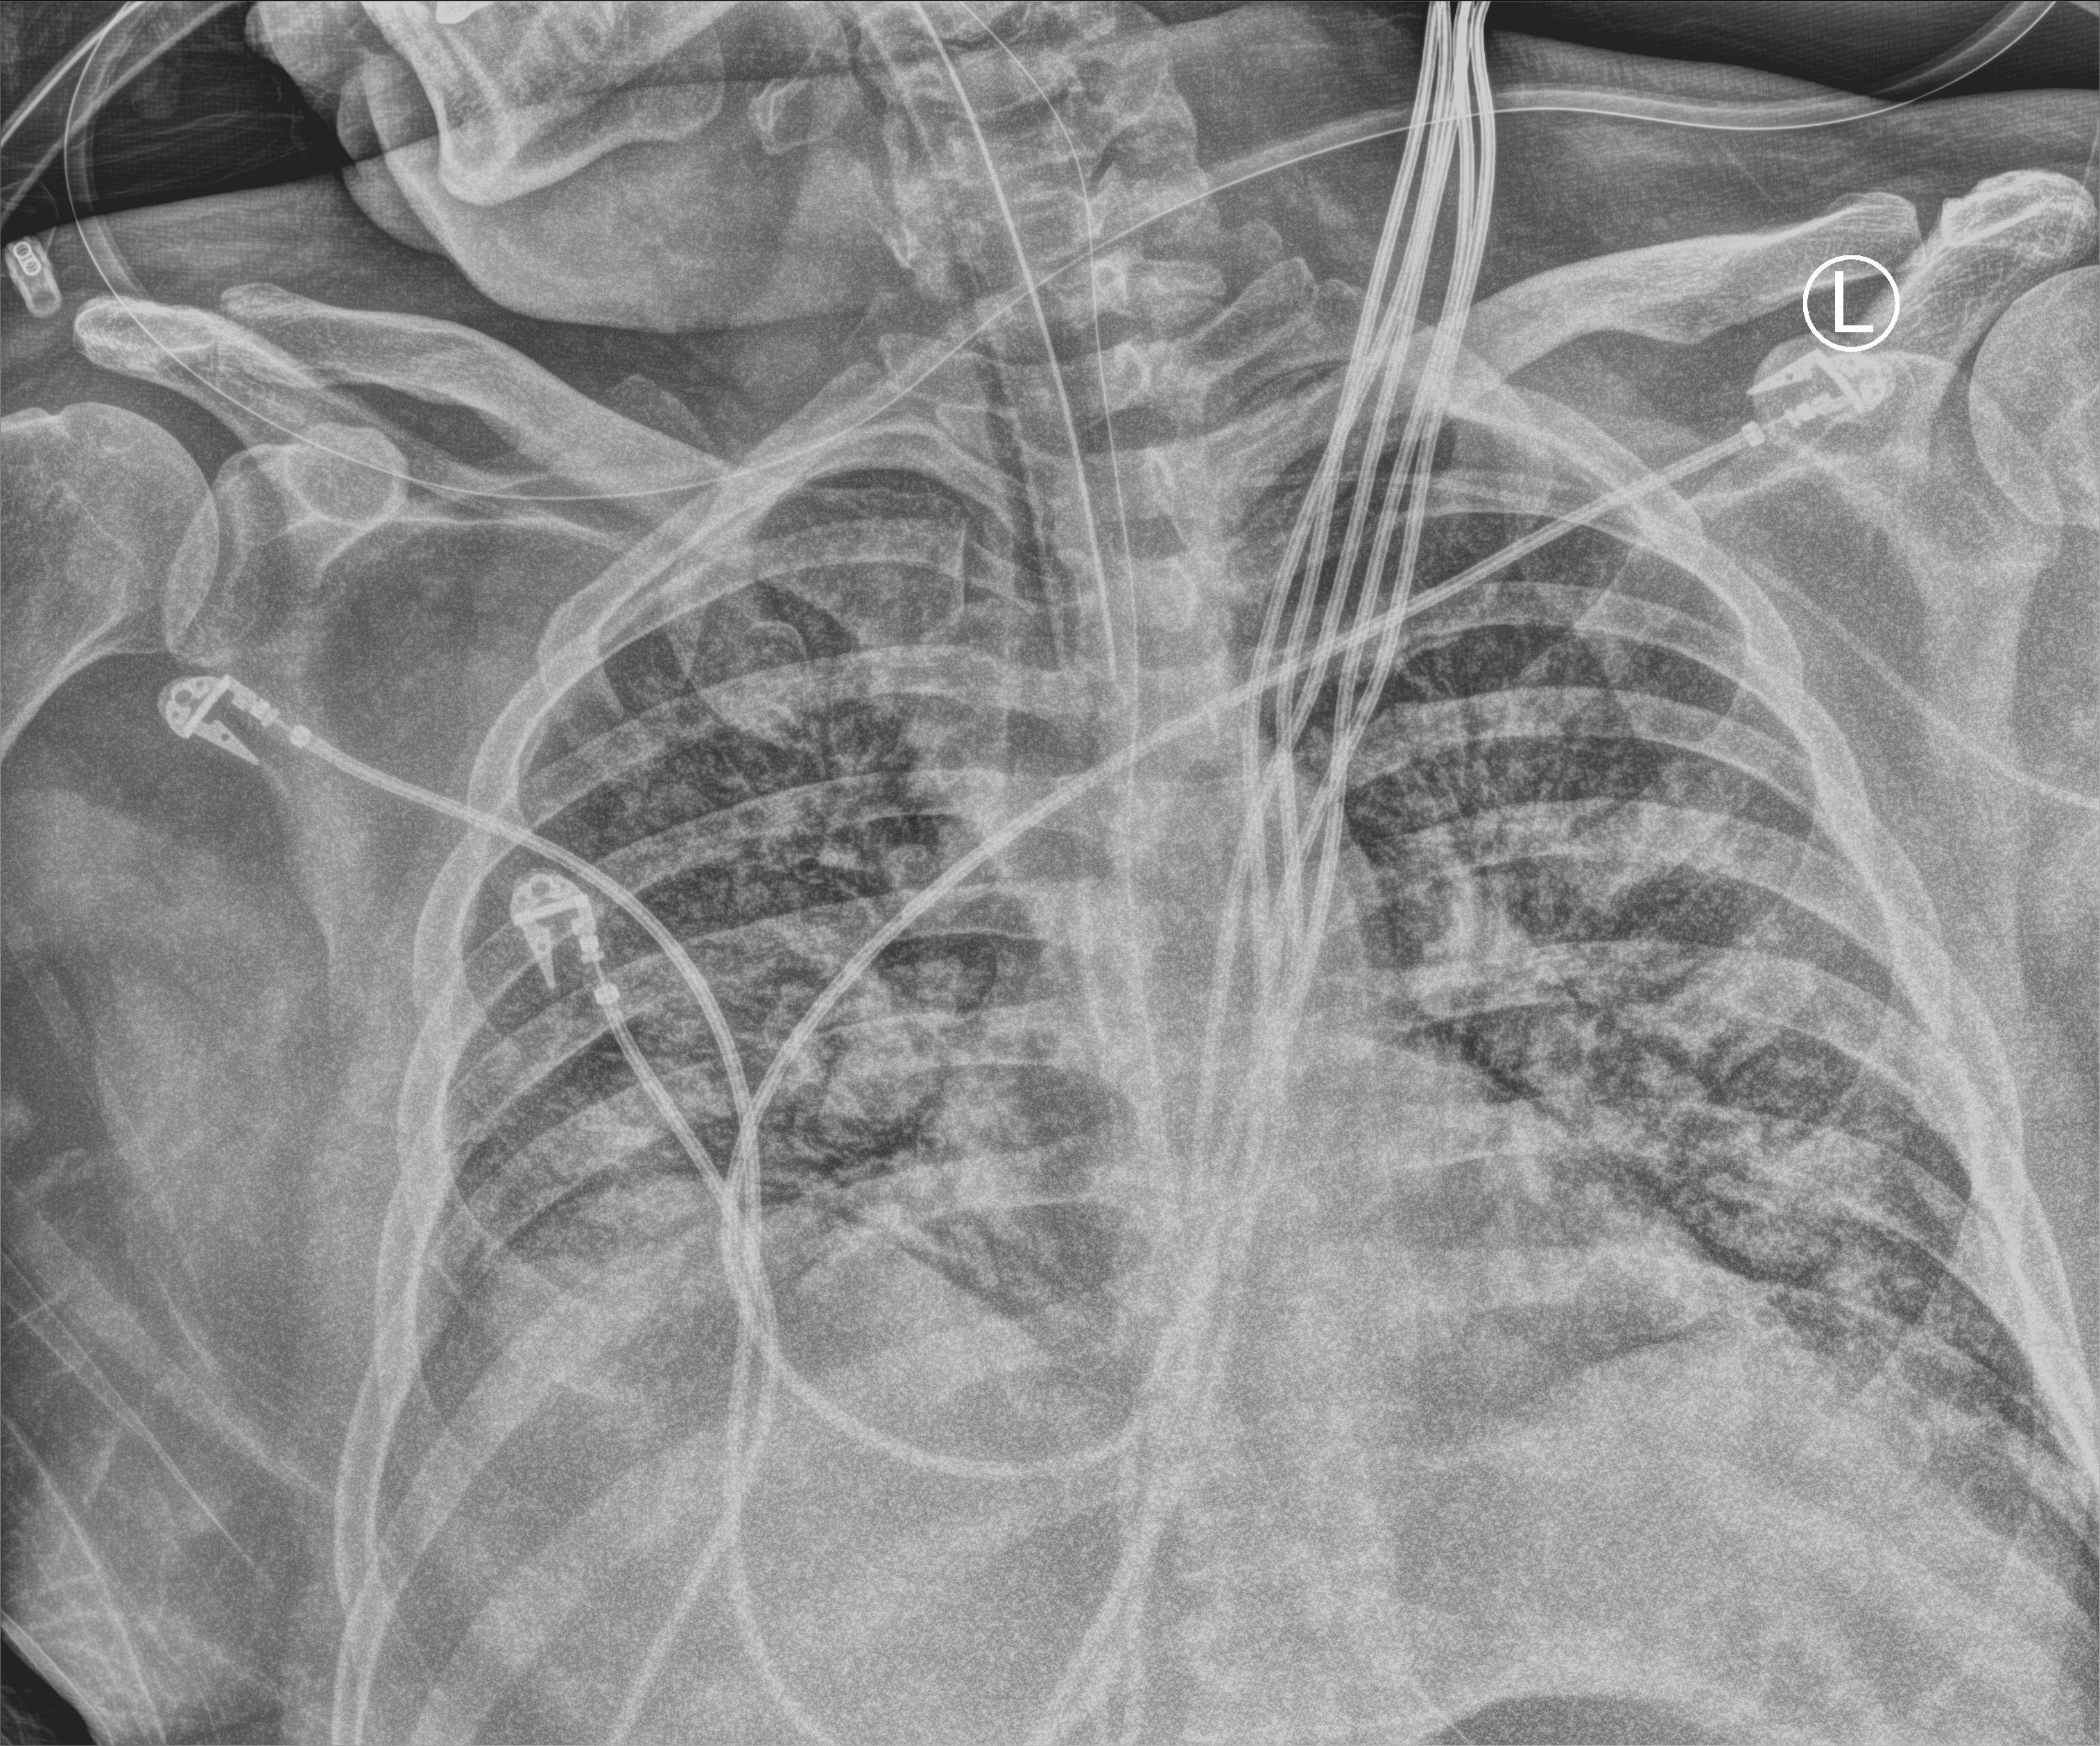
Chest X-ray (portable), anteroposterior (AP) projection. Patient hospitalised with COVID-19; male, aged 18–59 years.
From the hospital-stay record, not from the radiograph (when in the stay this image was taken is not recorded): chronic kidney disease (admission record): no; mechanically ventilated during this hospital stay: yes; admitted to intensive care during this hospital stay: yes.